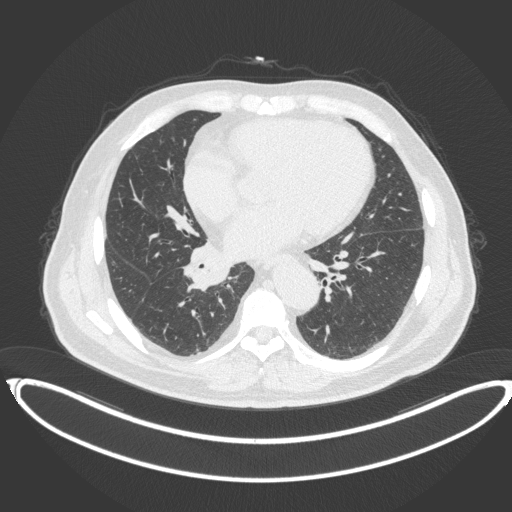
Chest CT, one axial slice. Position 178 of 383 along the scan axis. Reconstruction kernel B31f. Lung window (W 1500 / L -600 HU). 512 × 512 image matrix. Male patient, age 61 years. Case-level facts recorded for this patient, not image findings: clinical TNM (as recorded): T1b N1 M0.
Outlined on this slice (bounding box drawn by a radiologist):
- lung tumour (recorded histology: squamous cell carcinoma): box from (x=182, y=241) to (x=231, y=293) px